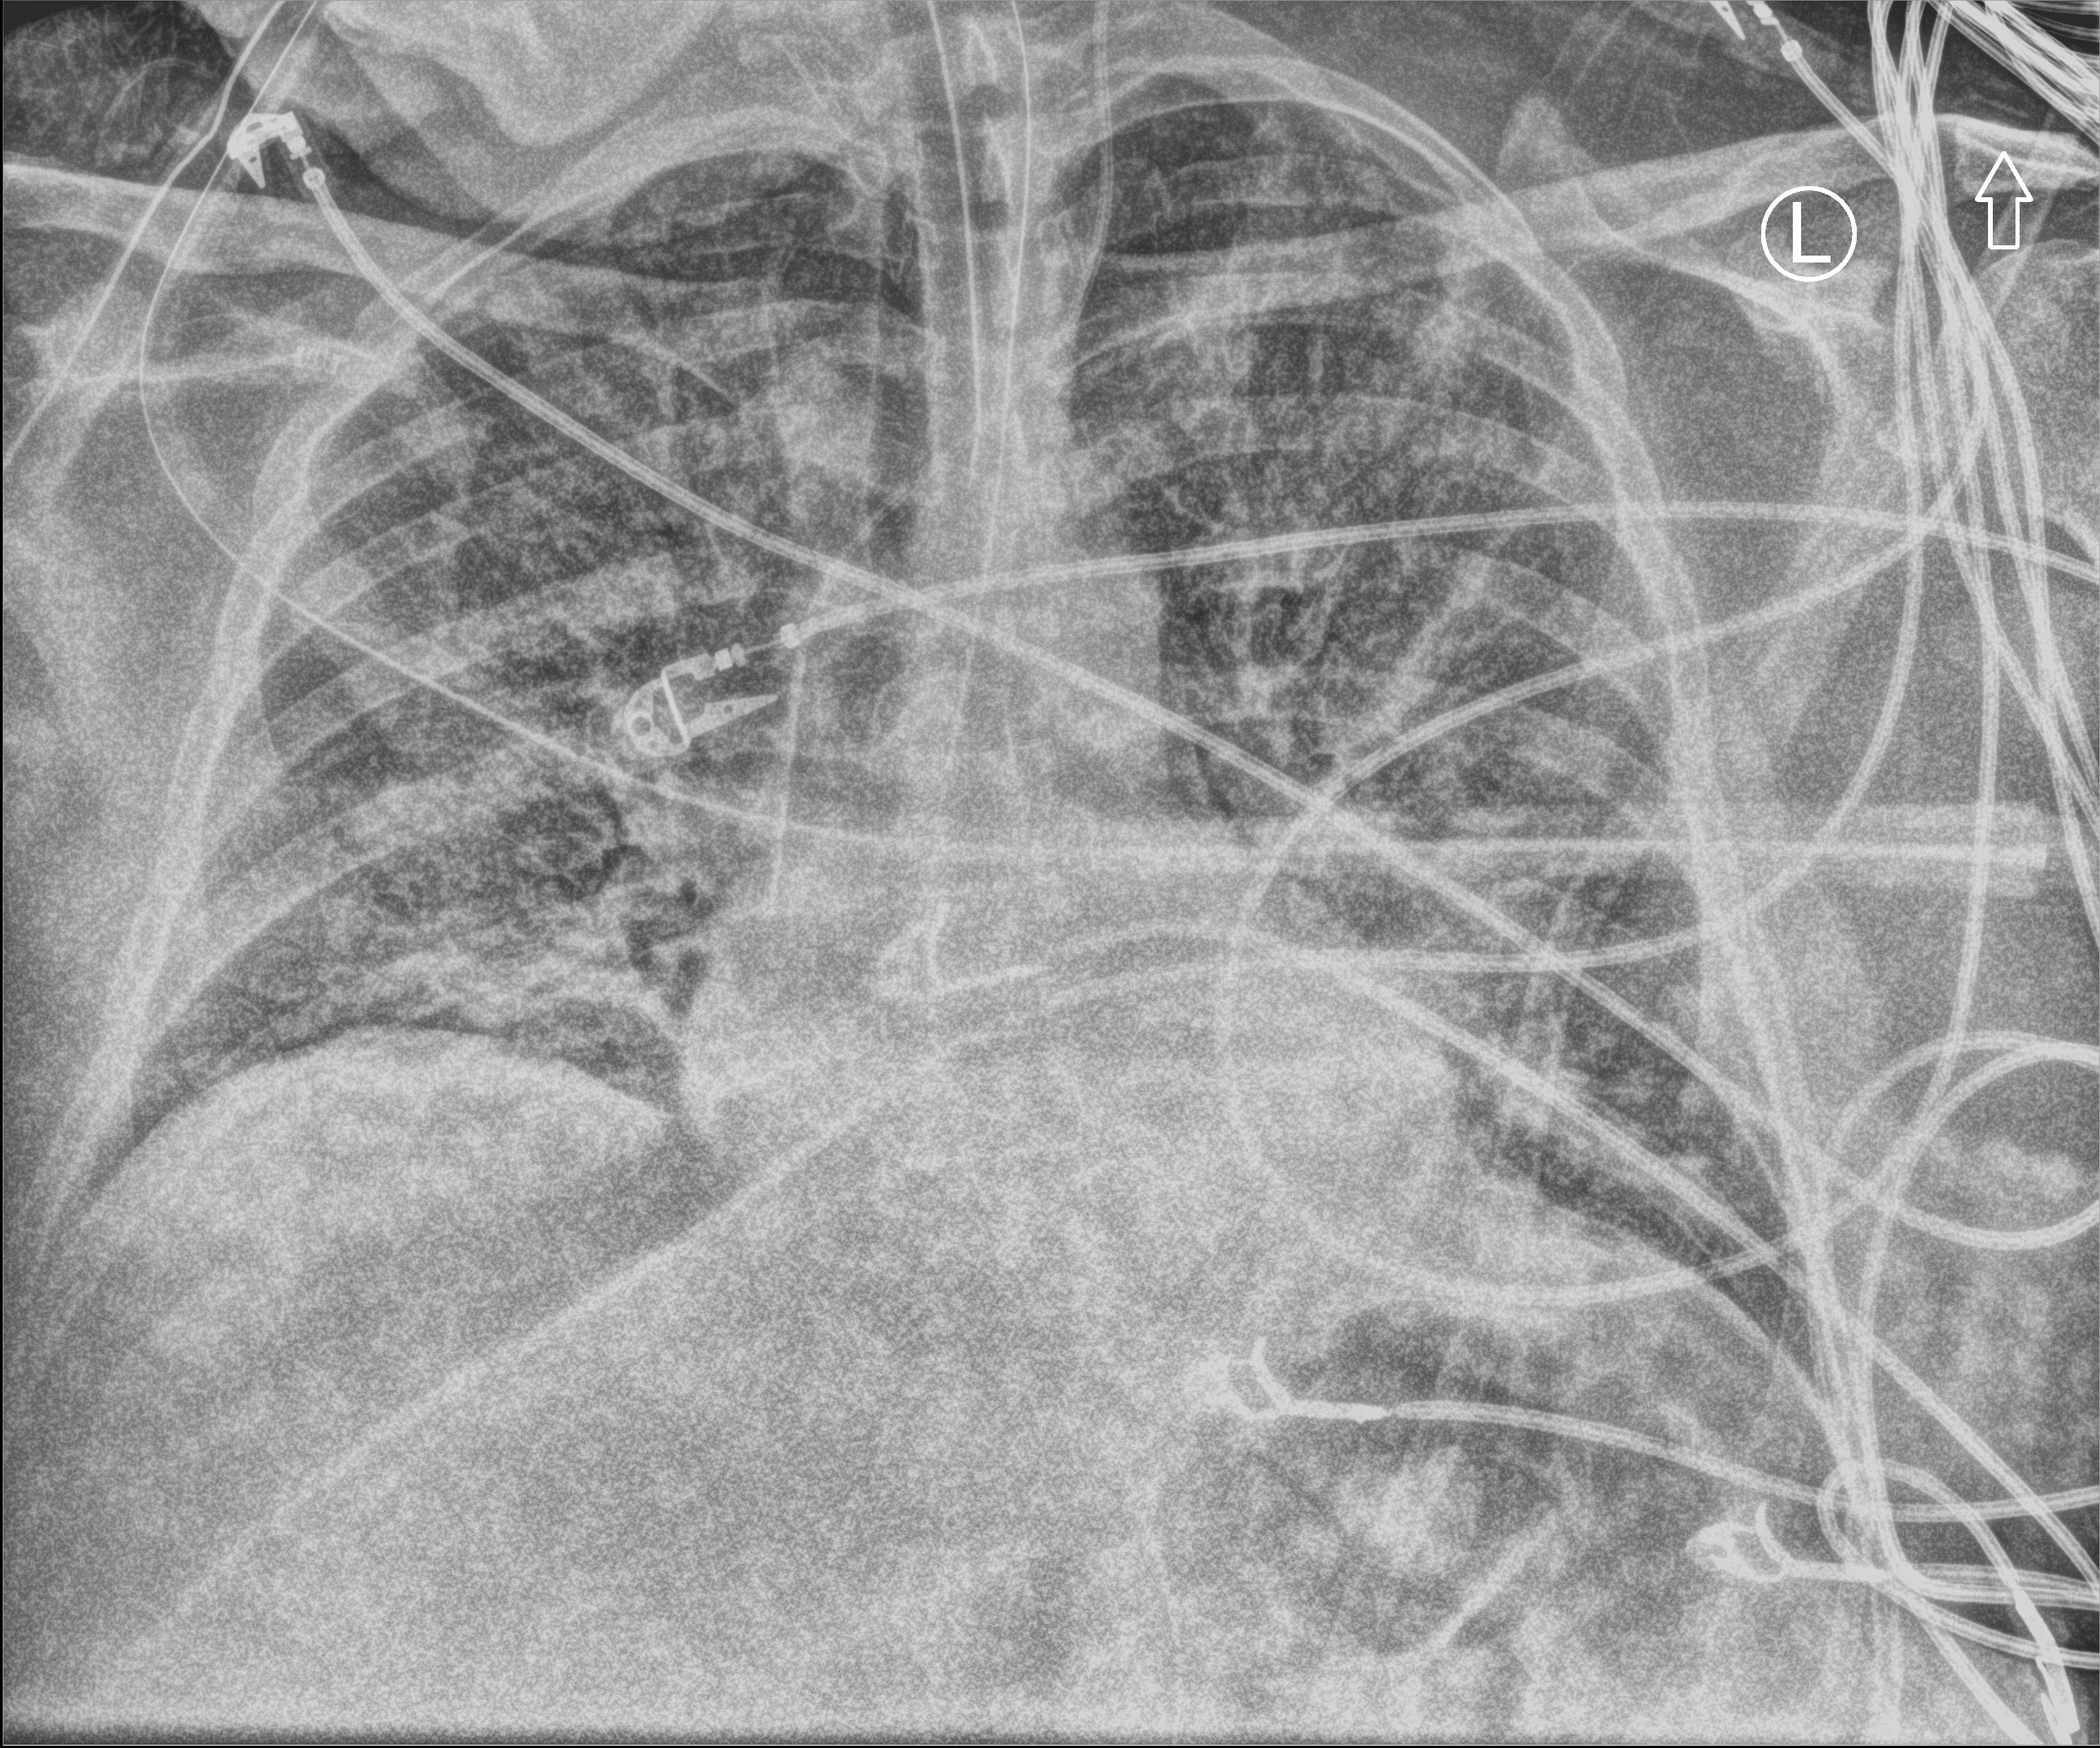
Chest X-ray (portable), anteroposterior (AP) projection. Patient hospitalised with COVID-19, aged 18–59 years.
Admission-level facts for this patient (not findings on this image; timing relative to this image not recorded):
- mechanically ventilated during this hospital stay: yes